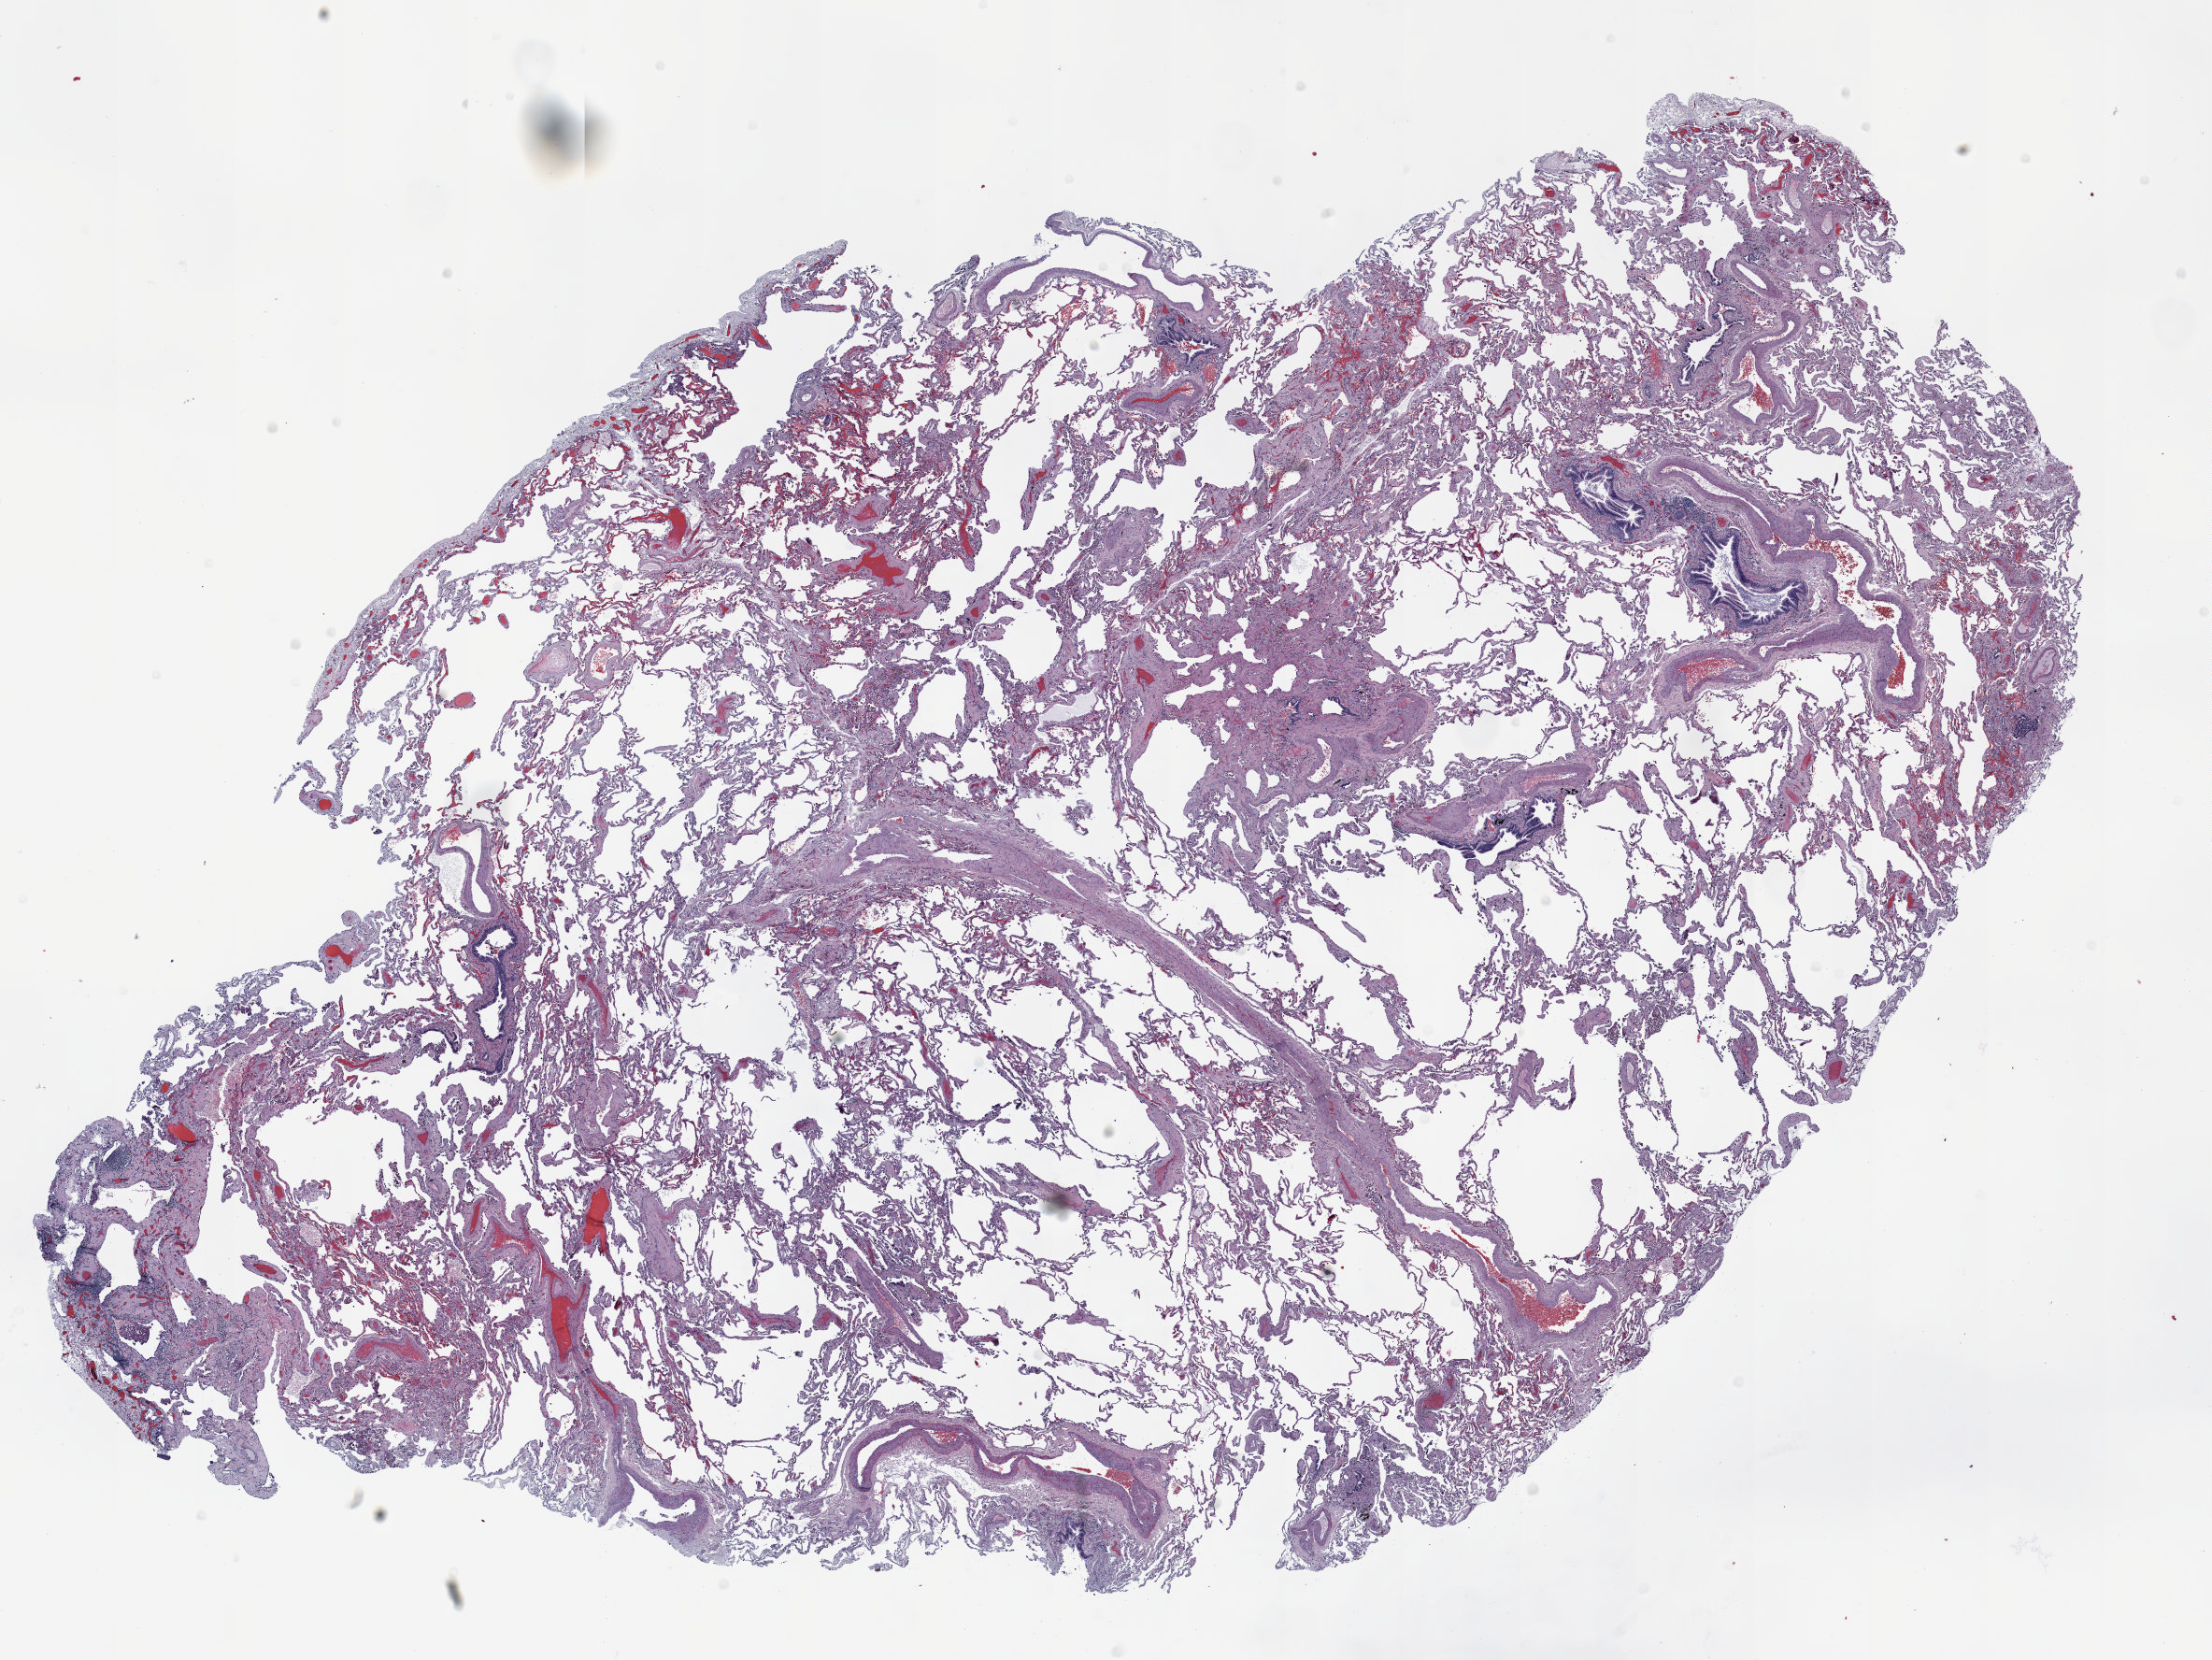
Hematoxylin and eosin (H&E) stained whole-slide image, whole scanned area (about 19.0 x 14.3 mm, slide scanned at 20x) shown as a low-resolution overview, formalin-fixed paraffin-embedded (FFPE) section, lung. Female, age 60 at enrolment. Grade: well differentiated (G1).
* tumour size (pathology): 11 mm
* participant's lung-cancer diagnosis: Bronchiolo-alveolar adenocarcinoma, NOS
* primary tumour location (clinical record): right upper lobe
* stage (AJCC 6th edition): IA